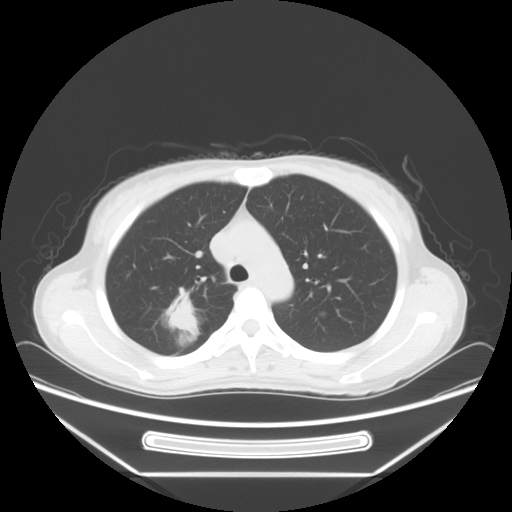
Chest CT, one axial slice; slice 48 of 66 in the series (ordered by position); lung window (W 1500 / L -600 HU); 5 mm slice thickness; 512 × 512 image matrix, field of view 408 × 408 mm. Female patient, age 37 years. From the clinical record (not read from this slice): clinical TNM (as recorded): T1c N0 M1.
Outlined on this slice (rectangle marked by the reading radiologist):
- lung tumour (recorded histology: adenocarcinoma): bounding box <167,277,198,342> (left, top, right, bottom; pixels)